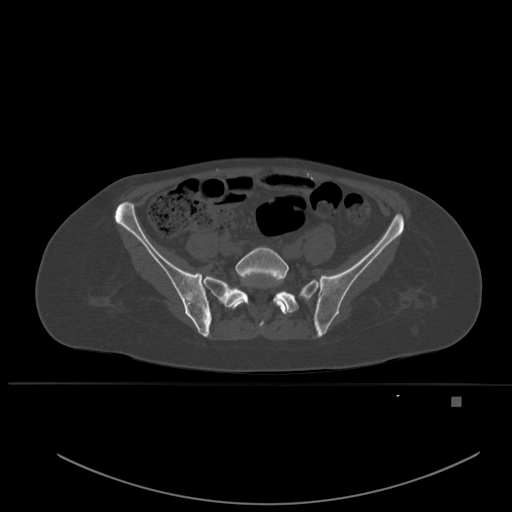
CT including the spine, one axial slice; position 145 of 651 along the scan axis; bone window (W 1800 / L 400 HU); 1.5 mm slice thickness; 512 × 512 image matrix, field of view 443 × 443 mm. Patient: female, 49 years. From the clinical record (not read from this slice): primary cancer: breast.
Outlined on this slice (semi-automatically segmented with operator editing):
- L5 vertebra: bounding box <231,247,291,315> (left, top, right, bottom; pixels)